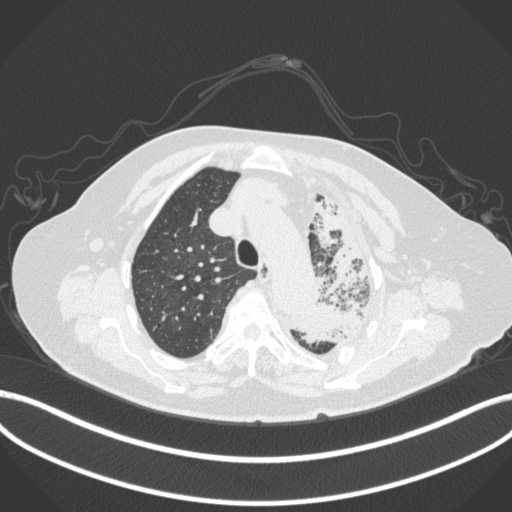
Chest CT, one axial slice. Slice 300 of 399 in the series (ordered by position). Reconstruction kernel B31f. 120 kVp. Lung window (W 1500 / L -600 HU). 1 mm slice thickness. 512 × 512 image matrix, field of view 400 × 400 mm. Patient: female, 75 years. Case-level facts recorded for this patient, not image findings: clinical TNM (as recorded): T3 N3 M1.
Annotated regions visible in this slice (bounding box drawn by a radiologist):
- lung tumour (recorded histology: adenocarcinoma): bounding box (x1, y1, x2, y2) in pixels: (288, 195, 378, 346)